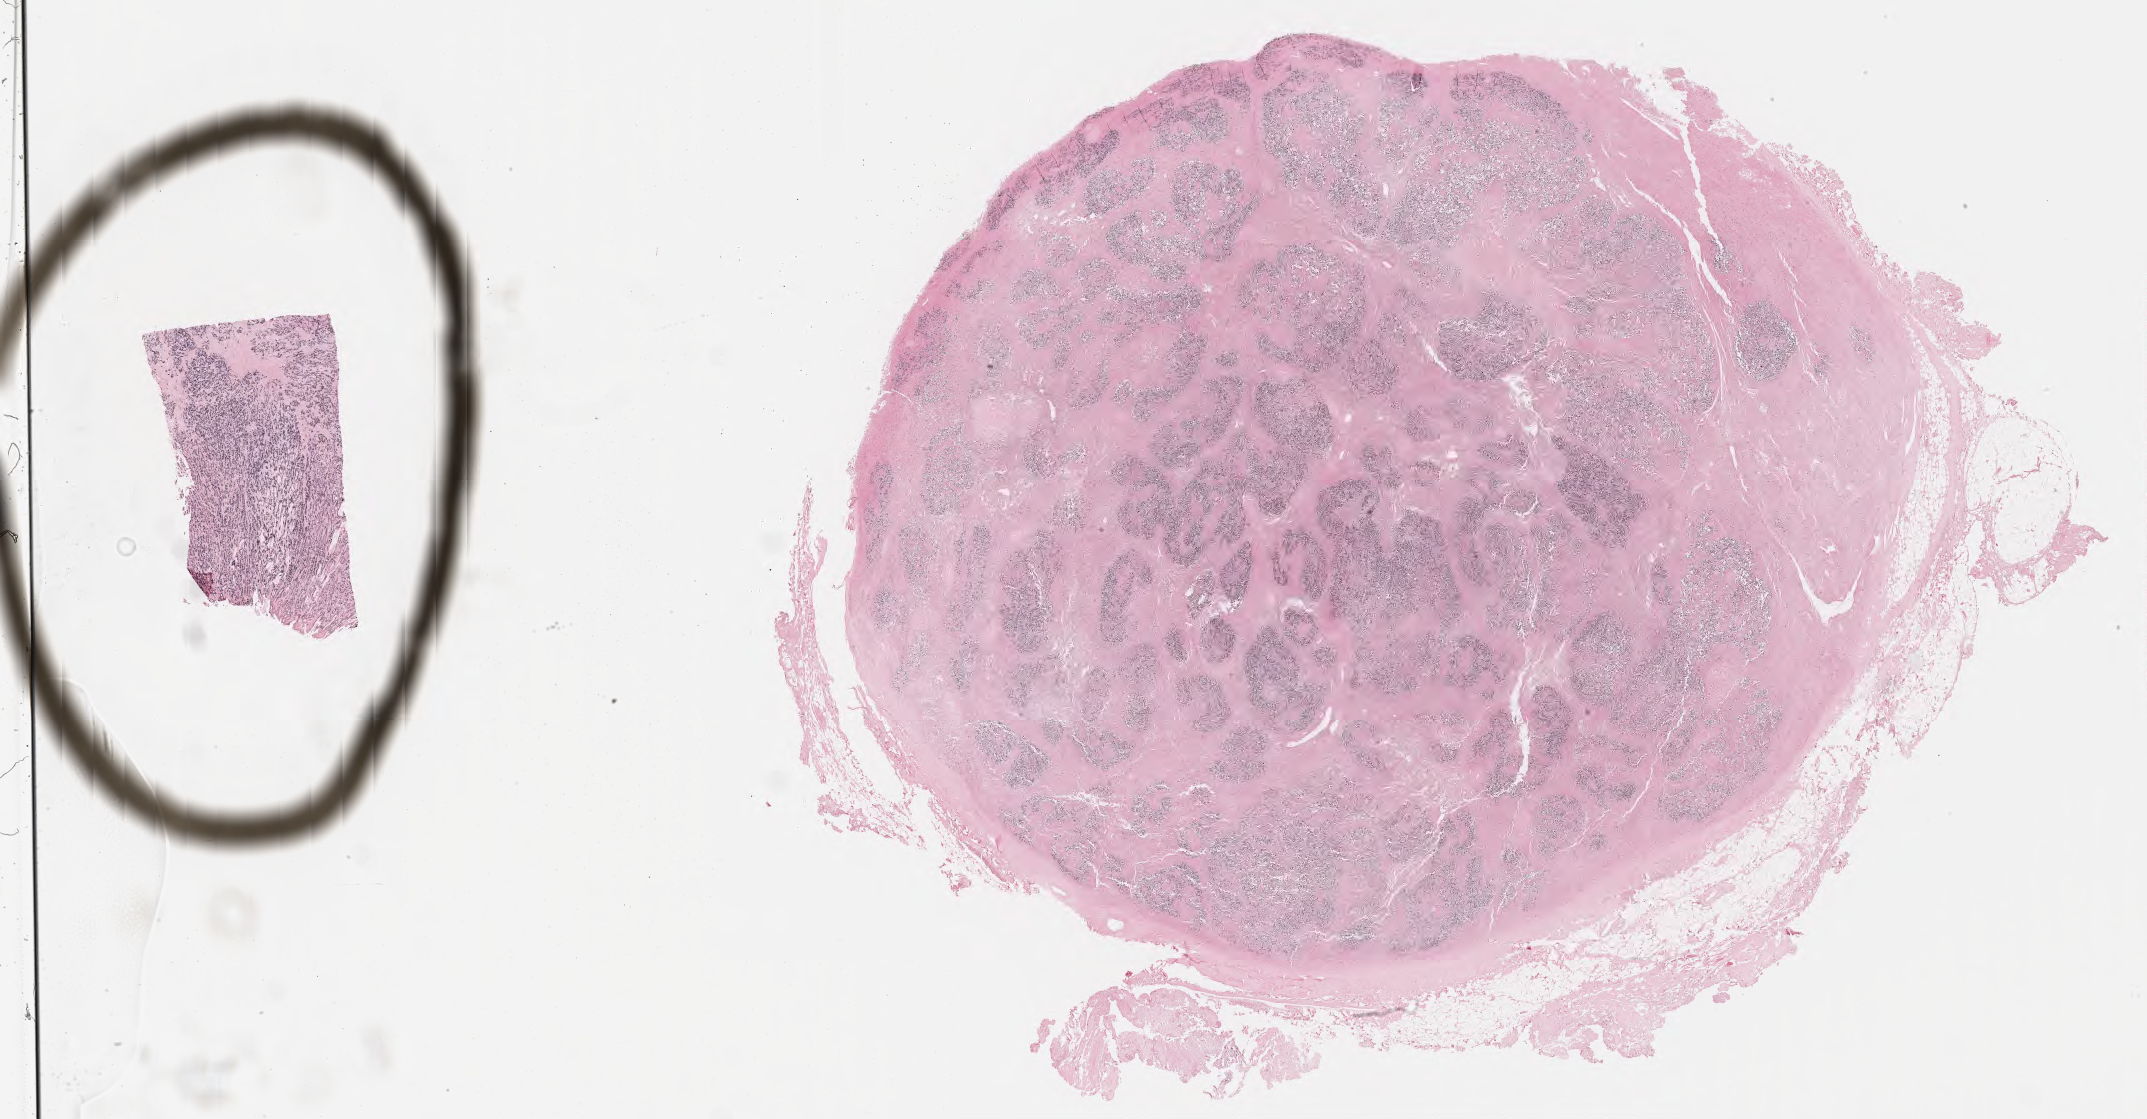
In-situ hybridisation whole-slide image, Epstein–Barr virus-encoded RNA (EBER) probe, shown as a low-resolution overview of the whole scanned area (about 34.7 x 18.1 mm); tumor tissue; site: lymph node. Patient male; 46 years old.
Diagnosis: Diffuse large B-cell lymphoma, NOS.